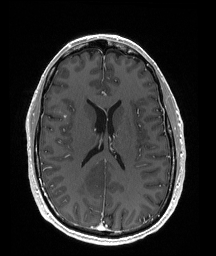
Brain MRI from a brain-tumour surgery series, one axial slice; slice 79 of 176 in the series (ordered by position); T1-weighted post-contrast; 1 mm slice thickness; 216 × 256 image matrix. From the clinical record (not read from this slice): histopathology: Oligodendroglioma; WHO grade: 2; IDH mutation: yes; tumour location: Right Parietal.
Outlined on this slice (manually delineated by an expert):
- tumour: bounding box [x1, y1, x2, y2] px = [70, 166, 111, 195]